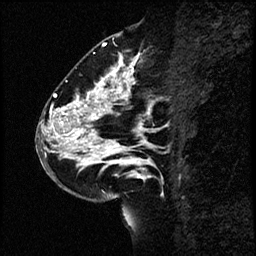
Breast MRI (dynamic contrast-enhanced), one sagittal slice; slice 31 of 60 in the series (ordered by position); dynamic contrast-enhanced study with each time point stored as its own series, time point 2 of 4 at this slice position (early post-contrast, ordered by acquisition time); 1.5 T; TE 4.2 ms, TR 17.6 ms; 256 × 256 image matrix, field of view 200 × 200 mm. Female patient, age 43 years. Case-level facts recorded for this patient, not image findings: setting: breast cancer imaged before/during neoadjuvant chemotherapy.
Outlined on this slice (semi-automatic segmentation, software-assisted and operator-edited):
- analysis volume of interest (the breast-tissue region the enhancement analysis was run in; not a lesion): box from (x=38, y=56) to (x=169, y=191) px
- tumour enhancement mask (voxels above the 100 % enhancement threshold inside the analysis volume of interest): (x=41, y=56)–(x=154, y=177)